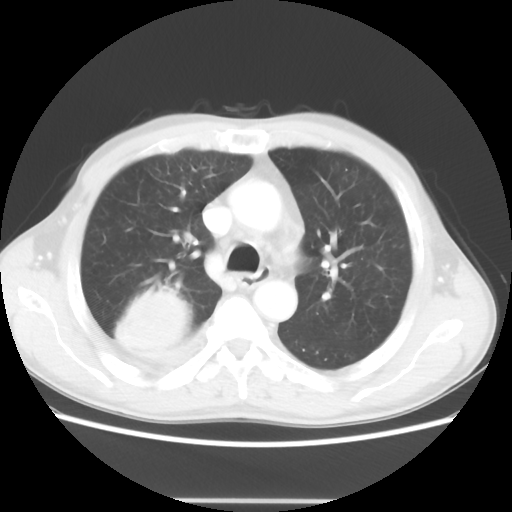
Chest CT, one axial slice. Position 34 of 48 along the scan axis. Lung window (W 1500 / L -600 HU). 5 mm slice thickness. 512 × 512 image matrix. Male patient, age 66 years. Case-level facts recorded for this patient, not image findings: clinical TNM (as recorded): T4 N1 M1; histopathological grade: G3.
Annotated regions visible in this slice (rectangle marked by the reading radiologist):
- lung tumour (recorded histology: small cell carcinoma): box from (x=110, y=274) to (x=193, y=363) px